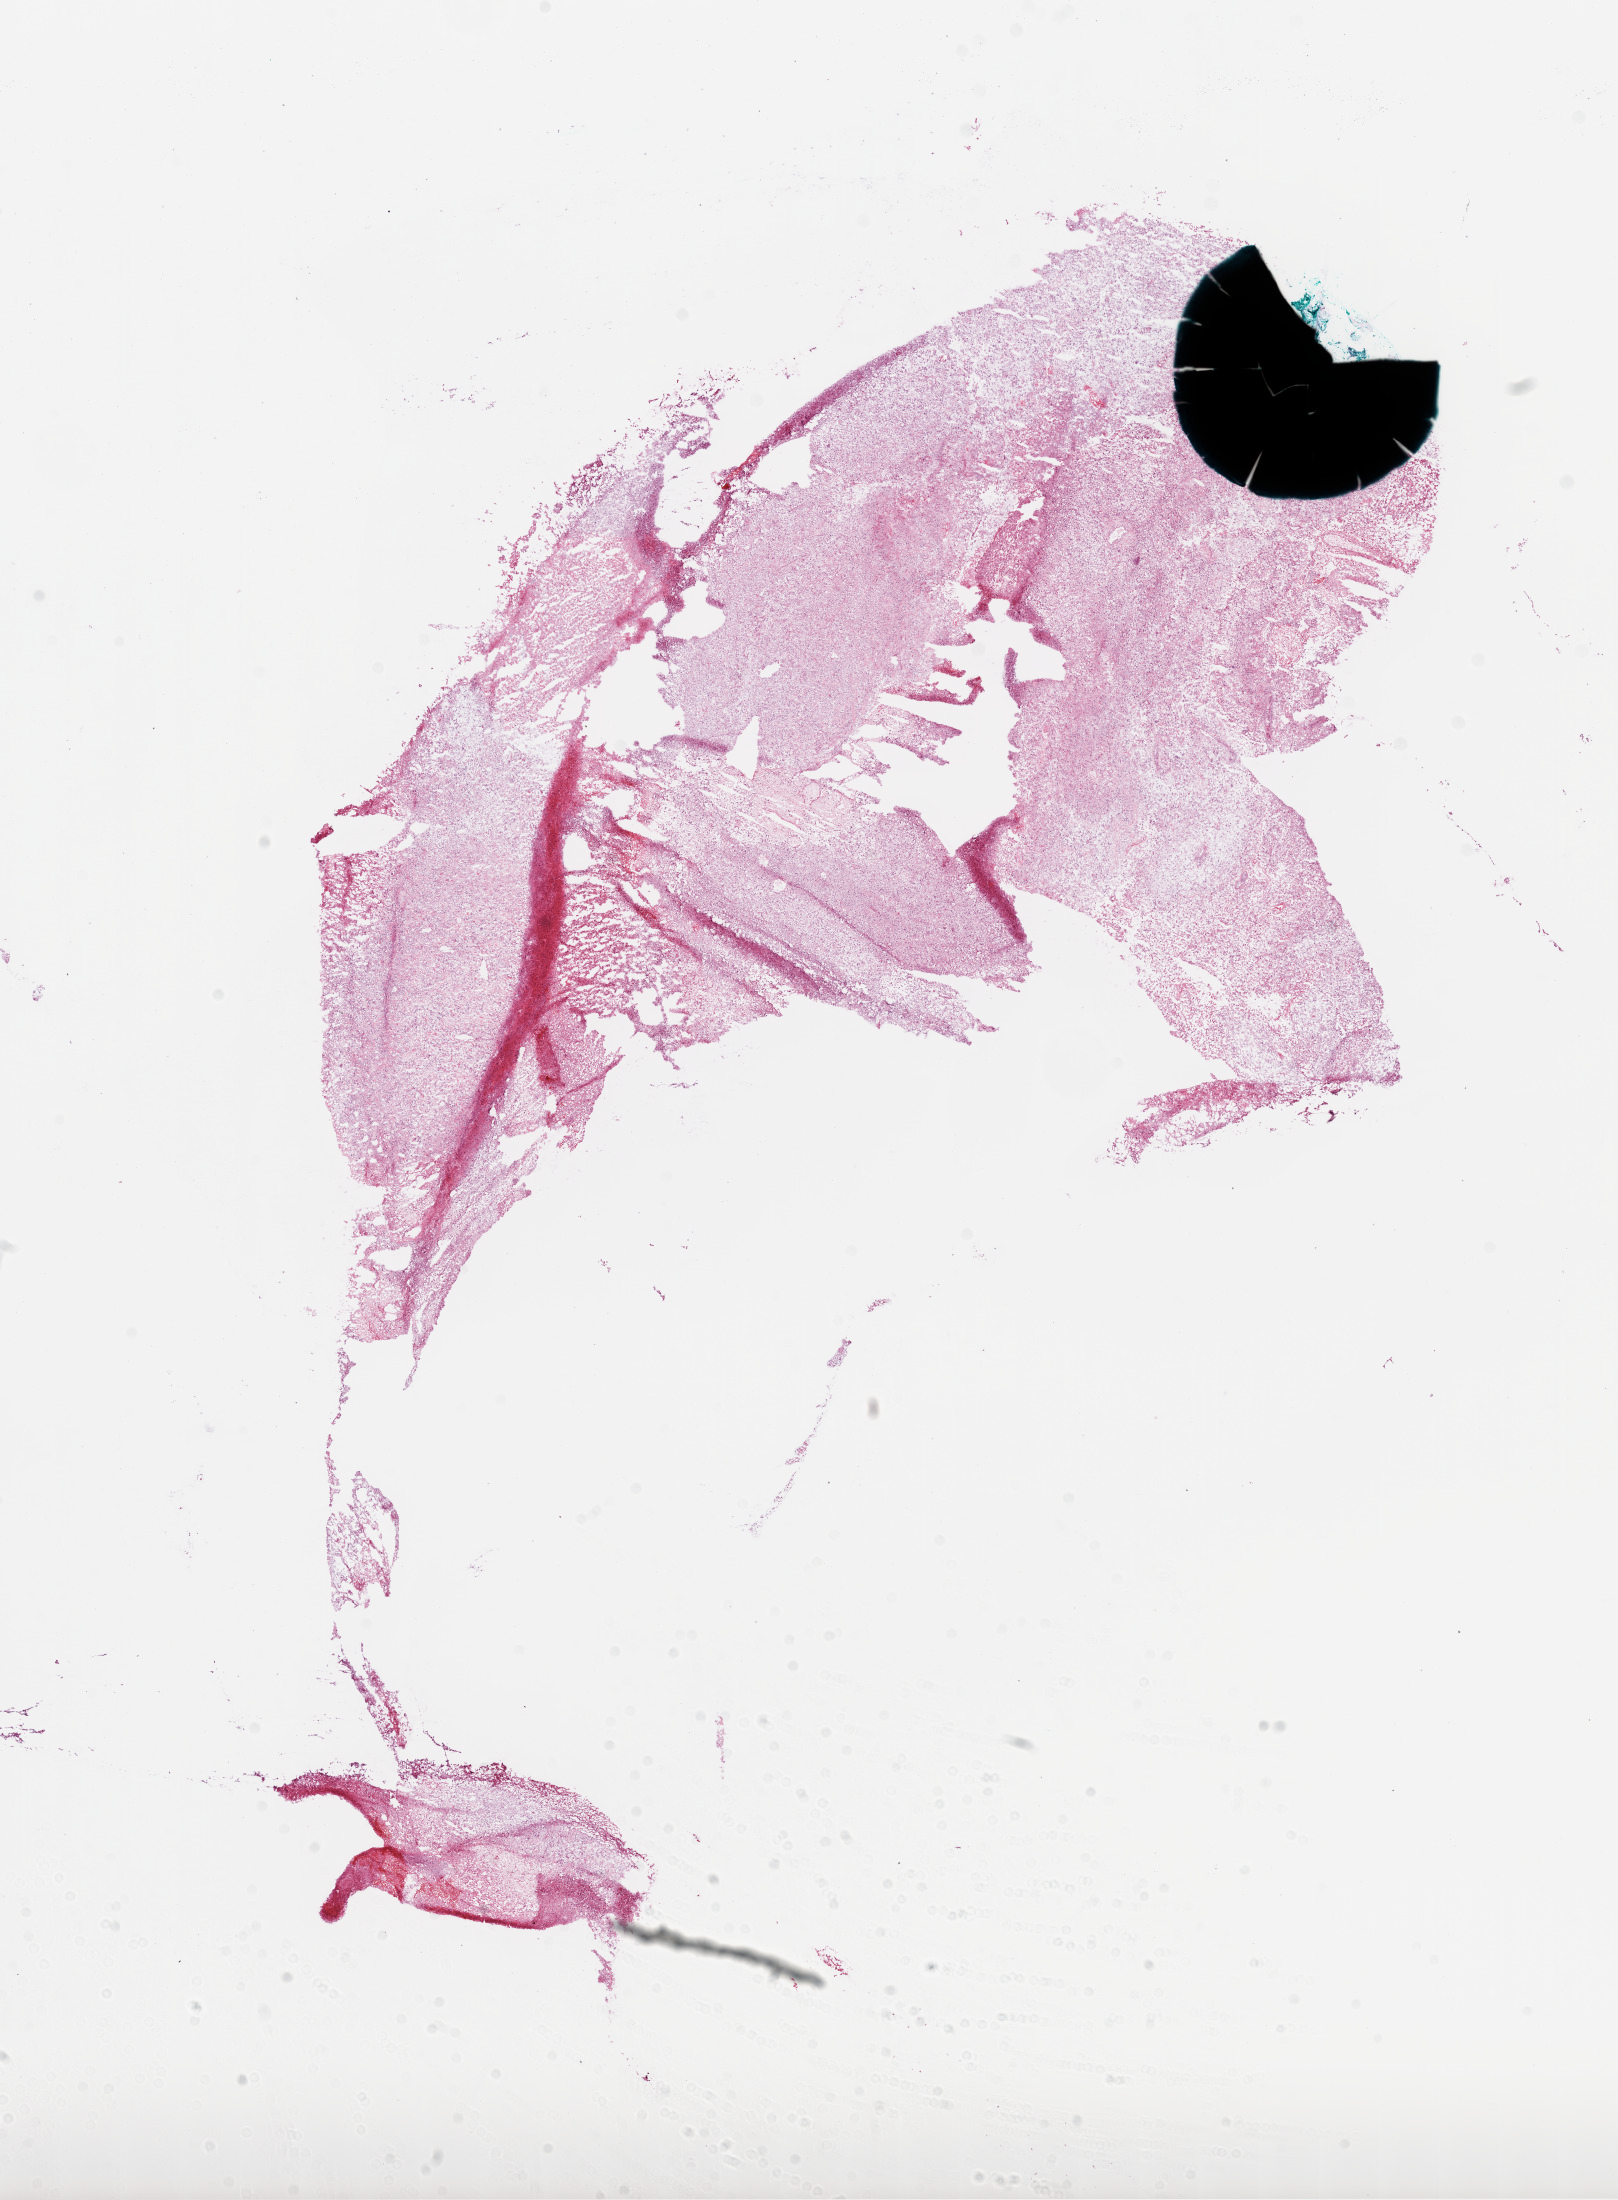
Digitized H&E-stained tissue section (whole slide), a low-resolution overview of the entire scanned area, about 13.1 x 17.7 mm. Frozen section. Sample: primary tumour, brain. Patient: female, age at initial diagnosis 60 years. Slide review estimates, as recorded: tumour cells 90%, tumour nuclei 100%, normal cells 0%, stromal cells 0%, necrosis 10%.
- diagnosis: Glioblastoma